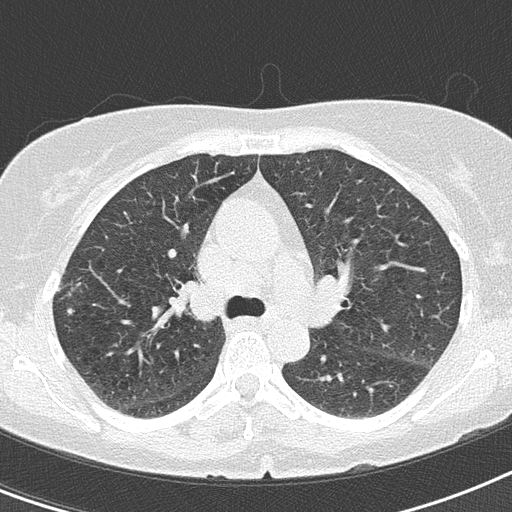
Low-dose screening chest CT, axial slice; second screening round (one year after baseline); lung window (W 1500 / L -600 HU); 2 mm slice thickness; lung (sharp) reconstruction kernel (B50f); 120 kVp; 512 × 512 image matrix, field of view 290 × 290 mm. Female participant, aged 61 years at enrolment. Current smoker at enrolment.
Lesion marked by an expert reader, box from (x=50, y=288) to (x=94, y=336) px. Screening reader's record for this exam: no non-calcified nodule ≥4 mm recorded. Official screen result: negative screen, significant abnormalities not suspicious for lung cancer. Participant outcome: lung cancer diagnosed 125 days after this screen — small cell carcinoma, NOS, right upper lobe, stage IIIA (AJCC 6th edition), 7 mm at pathology.